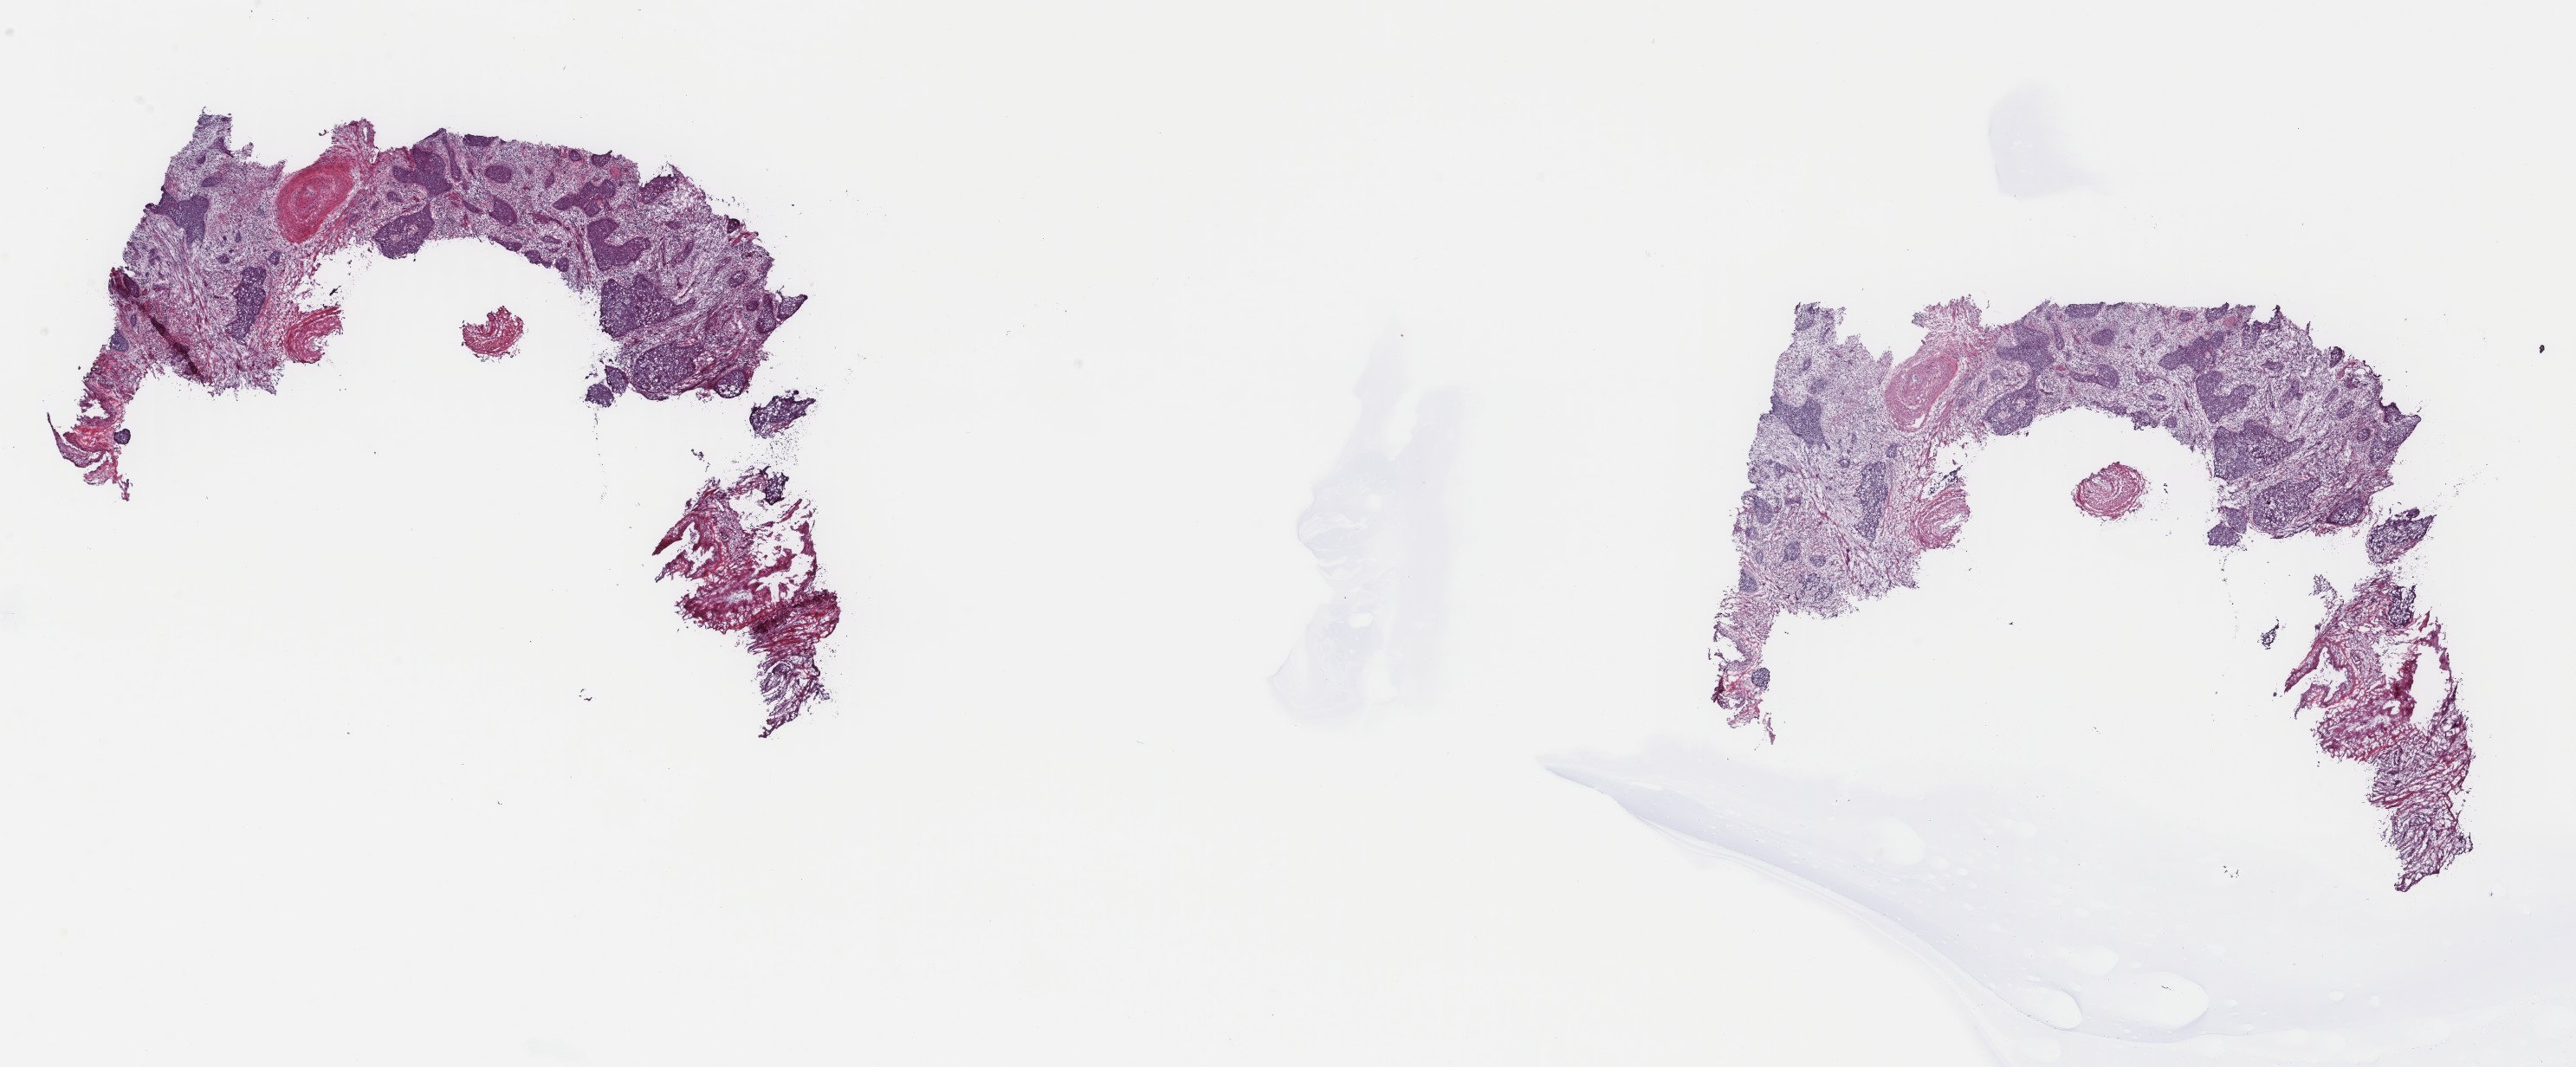
Whole-slide histology image, H&E-stained — a low-resolution overview of the entire scanned area, about 23.6 x 9.8 mm. Frozen section. Cervix, primary tumour sample. Female patient; age at initial diagnosis 40 years. Histologic grade: G3 (poorly differentiated). Slide review estimates, as recorded: tumour cells 80%, tumour nuclei 60%, normal cells 10%, stromal cells 10%, necrosis 0%. Inflammatory infiltration, as recorded: lymphocyte infiltration 5%, monocyte infiltration 0%, neutrophil infiltration 1%.
* lymph nodes positive (case pathology): 4 of 41 examined
* histologic diagnosis: Squamous cell carcinoma, NOS (cervix uteri)
* FIGO stage: IB1